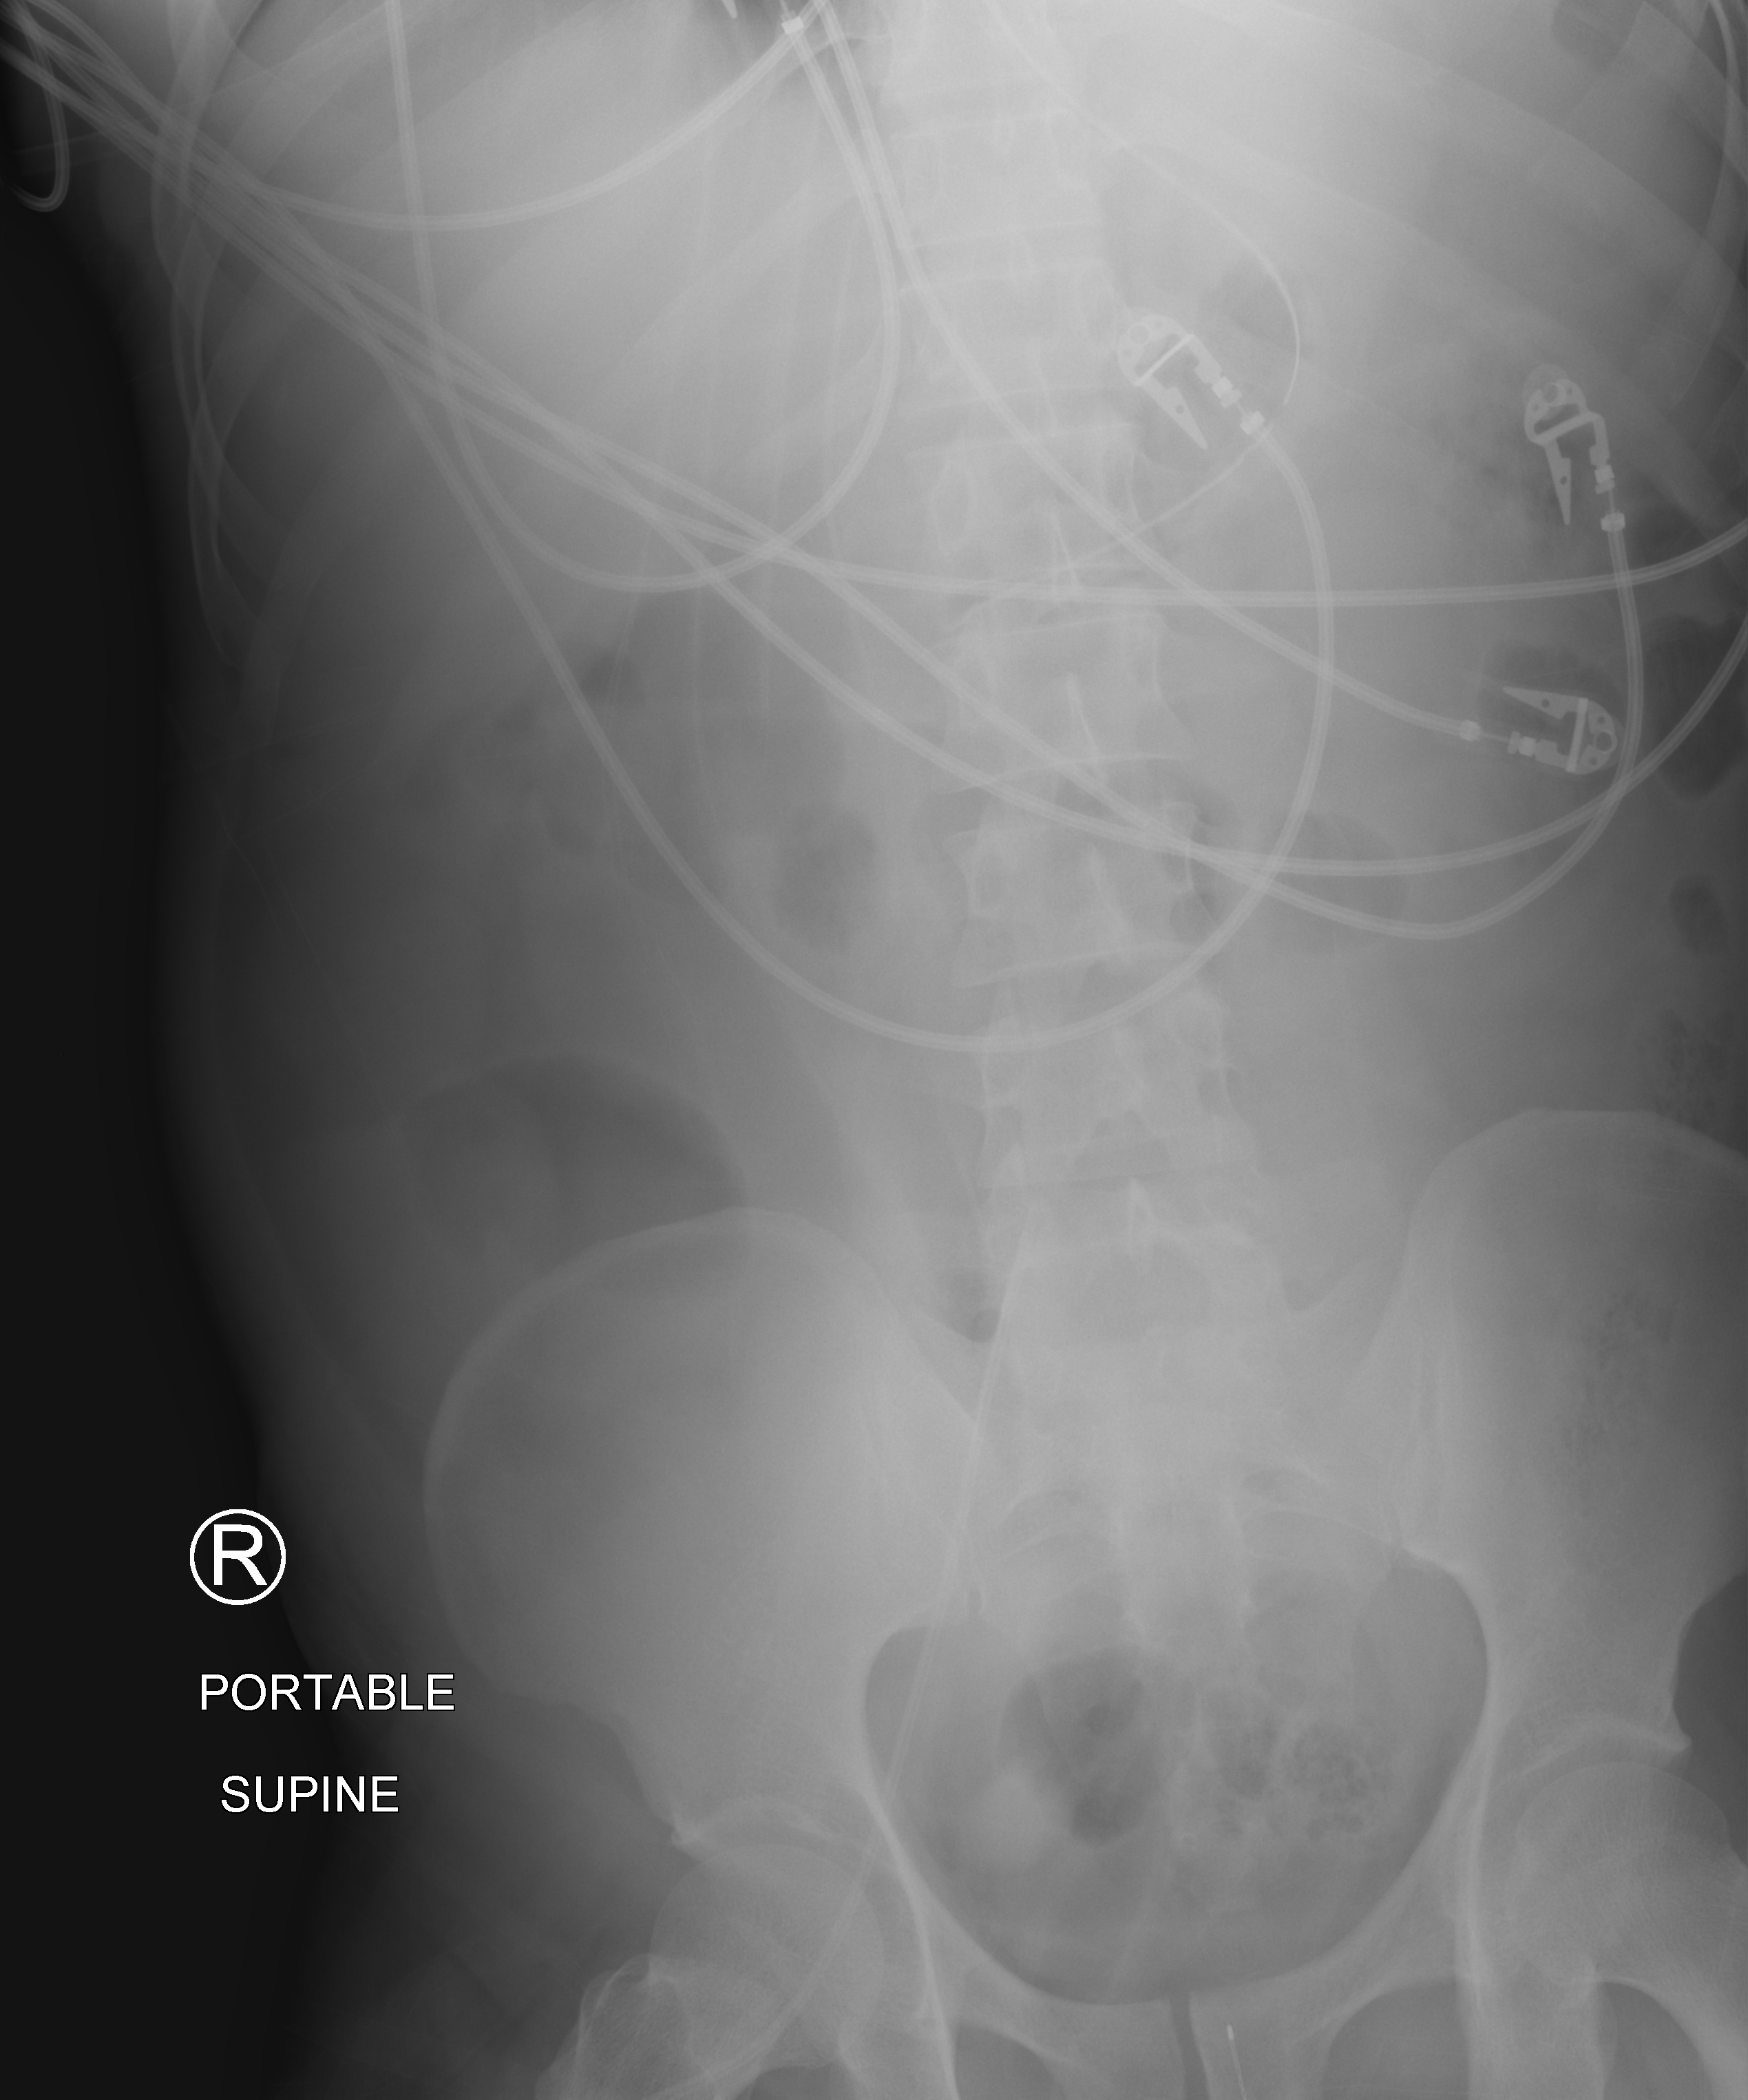
Portable abdomen radiograph, anteroposterior (AP) projection. Patient hospitalised with COVID-19; male, aged 18–59 years.
From the hospital-stay record, not from the radiograph (when in the stay this image was taken is not recorded):
- admitted to intensive care during this hospital stay: yes
- other chronic lung disease (admission record): no
- mechanically ventilated during this hospital stay: yes